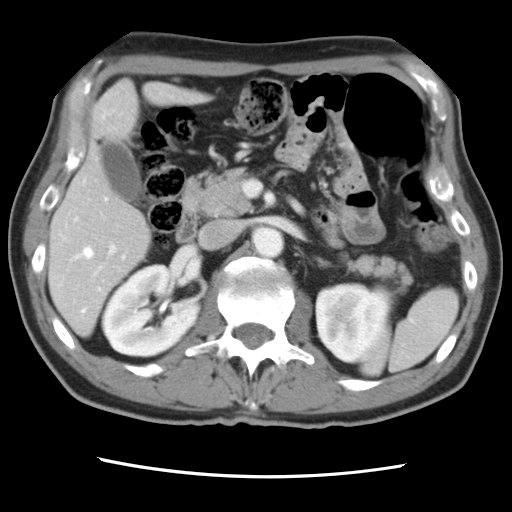
Contrast-enhanced abdominal CT, one axial slice; slice 40 of 83 in the series (ordered by position); 120 kVp; intravenous contrast given; soft-tissue window (W 400 / L 40 HU); 5 mm slice thickness; 512 × 512 image matrix, field of view 321 × 321 mm. Male patient, age 69 years. Case-level facts recorded for this patient, not image findings: diagnosis: colorectal cancer liver metastases, imaged before liver resection; multiple liver metastases: yes; largest metastasis: 3.5 cm; chemotherapy before resection: yes.
Outlined on this slice (manually delineated by an expert):
- hepatic veins: bounding box <79,198,125,312> (left, top, right, bottom; pixels)
- liver: <51,82,201,334>
- planned liver remnant (the part of the liver to remain after resection): <51,151,151,334>
- portal vein (with intrahepatic branches): <73,179,117,277>